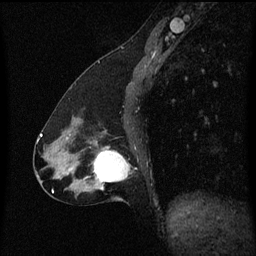
Breast MRI (dynamic contrast-enhanced), one sagittal slice; position 26 of 60 along the scan axis; dynamic contrast-enhanced series, image 2 of 3 at this slice position (ordered by acquisition); 1.5 T; TE 4.2 ms, TR 8.4 ms; 2 mm slice thickness; 256 × 256 image matrix. Patient: female, 47 years.
Annotated regions visible in this slice (semi-automatically segmented with operator editing):
- analysis volume of interest (the breast-tissue region the enhancement analysis was run in; not a lesion): box from (x=81, y=146) to (x=133, y=193) px
- tumour enhancement mask (voxels above the 70 % enhancement threshold inside the analysis volume of interest): (x=94, y=148)–(x=129, y=183)